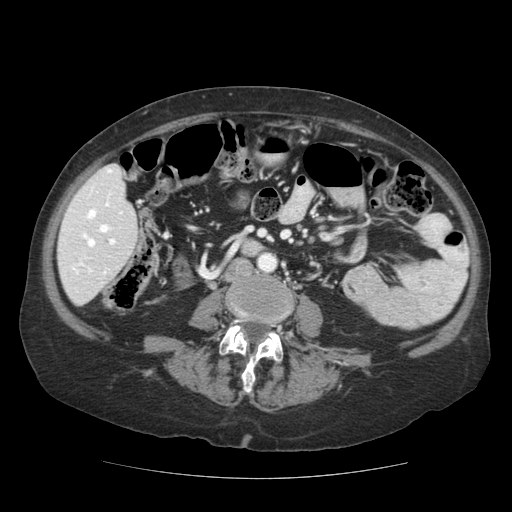
Contrast-enhanced abdominal CT (liver protocol), one axial slice; slice 38 of 111 in the series (ordered by position); 140 kVp; soft-tissue window (W 400 / L 40 HU); 512 × 512 image matrix. Case-level facts recorded for this patient, not image findings: diagnosis: hepatocellular carcinoma (patient treated with transarterial chemoembolisation; whether this scan precedes or follows treatment is not stated here); TNM stage (as recorded): Stage-I; Child-Pugh class: A.
Outlined on this slice (semi-automatic segmentation, software-assisted and operator-edited):
- liver parenchyma outside the tumour (the mass and vessels are separate outlines, so this box may not span the whole liver): bounding box <58,164,138,305> (left, top, right, bottom; pixels)
- liver vessels: <69,168,123,275>